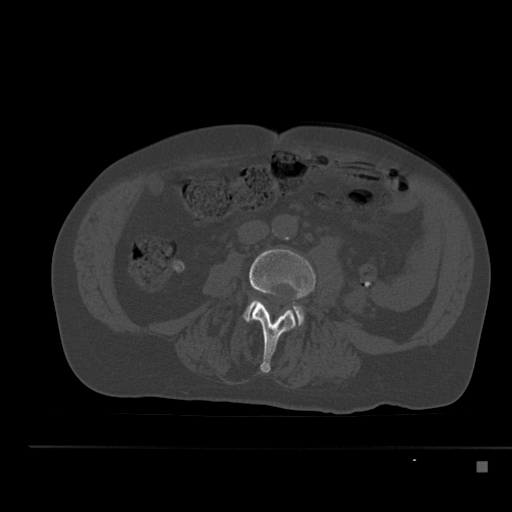
CT including the spine, one axial slice. Position 158 of 517 along the scan axis. Reconstruction kernel Br40s. Bone window (W 1800 / L 400 HU). 512 × 512 image matrix, field of view 408 × 408 mm. Patient: male, 70 years. Case-level facts recorded for this patient, not image findings: primary cancer: renal.
Annotated regions visible in this slice (semi-automatic segmentation, software-assisted and operator-edited):
- L3 vertebra: bounding box [x1, y1, x2, y2] px = [249, 249, 315, 373]
- L4 vertebra: [244, 301, 304, 325]